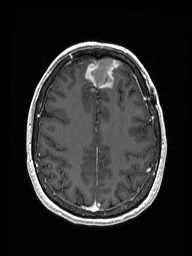
Brain MRI from a brain-tumour surgery series, one axial slice; position 54 of 192 along the scan axis; T1-weighted post-contrast; 1 mm slice thickness; 192 × 256 image matrix, field of view 187 × 250 mm. From the clinical record (not read from this slice): histopathology: Metastastic Carcinoma from Breast primary.
Annotated regions visible in this slice (expert manual segmentation):
- previous resection cavity: bounding box [x1, y1, x2, y2] px = [92, 58, 117, 86]